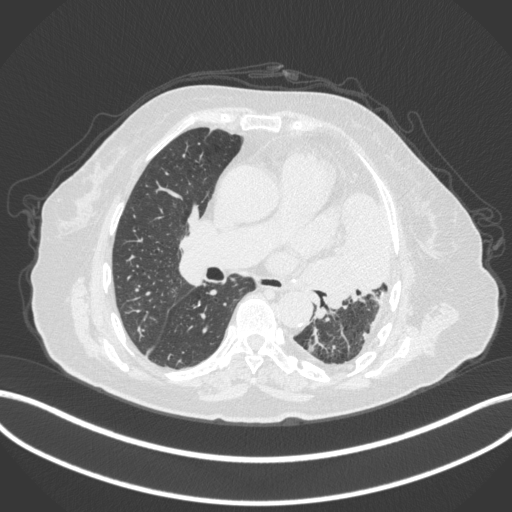
Chest CT, one axial slice; slice 201 of 399 in the series (ordered by position); reconstruction kernel B31f; 120 kVp; lung window (W 1500 / L -600 HU); 512 × 512 image matrix, field of view 400 × 400 mm. Female patient, age 75 years. From the clinical record (not read from this slice): clinical TNM (as recorded): T3 N3 M1.
Structures marked on this image (bounding box drawn by a radiologist):
- lung tumour (recorded histology: adenocarcinoma): bounding box (x1, y1, x2, y2) in pixels: (300, 190, 396, 311)